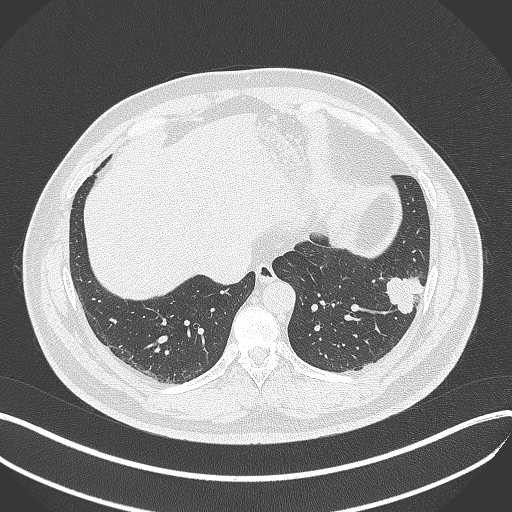
Chest CT, one axial slice; slice 120 of 429 in the series (ordered by position); reconstruction kernel B70f; 120 kVp; lung window (W 1500 / L -600 HU); 1 mm slice thickness; 512 × 512 image matrix. Male patient, age 39 years. From the clinical record (not read from this slice): clinical TNM (as recorded): T2a N0 M0; histopathological grade: G2-3.
Outlined on this slice (rectangle marked by the reading radiologist):
- lung tumour (recorded histology: adenocarcinoma): bounding box (x1, y1, x2, y2) in pixels: (382, 270, 430, 321)